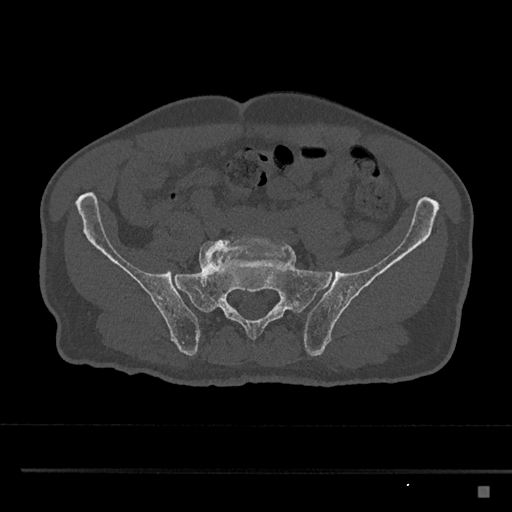
CT including the spine, one axial slice. Slice 538 of 797 in the series (ordered by position). Bone window (W 1800 / L 400 HU). 512 × 512 image matrix. Male patient, age 59 years. Case-level facts recorded for this patient, not image findings: primary cancer: prostate.
Outlined on this slice (semi-automatic segmentation, software-assisted and operator-edited):
- L5 vertebra: bounding box <199,235,291,271> (left, top, right, bottom; pixels)